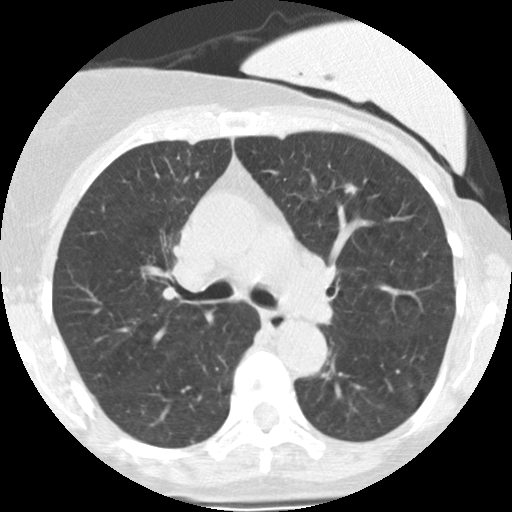
Low-dose screening chest CT, one axial slice; slice 159 of 251 in the series (ordered by position); reconstruction kernel STANDARD; 120 kVp; lung window (W 1500 / L -600 HU); 2.5 mm slice thickness; 512 × 512 image matrix, field of view 280 × 280 mm.
Annotated regions visible in this slice (manually delineated by an expert):
- lesion 1 (tumor, lower lobe of left lung): bounding box [x1, y1, x2, y2] px = [345, 185, 357, 194]